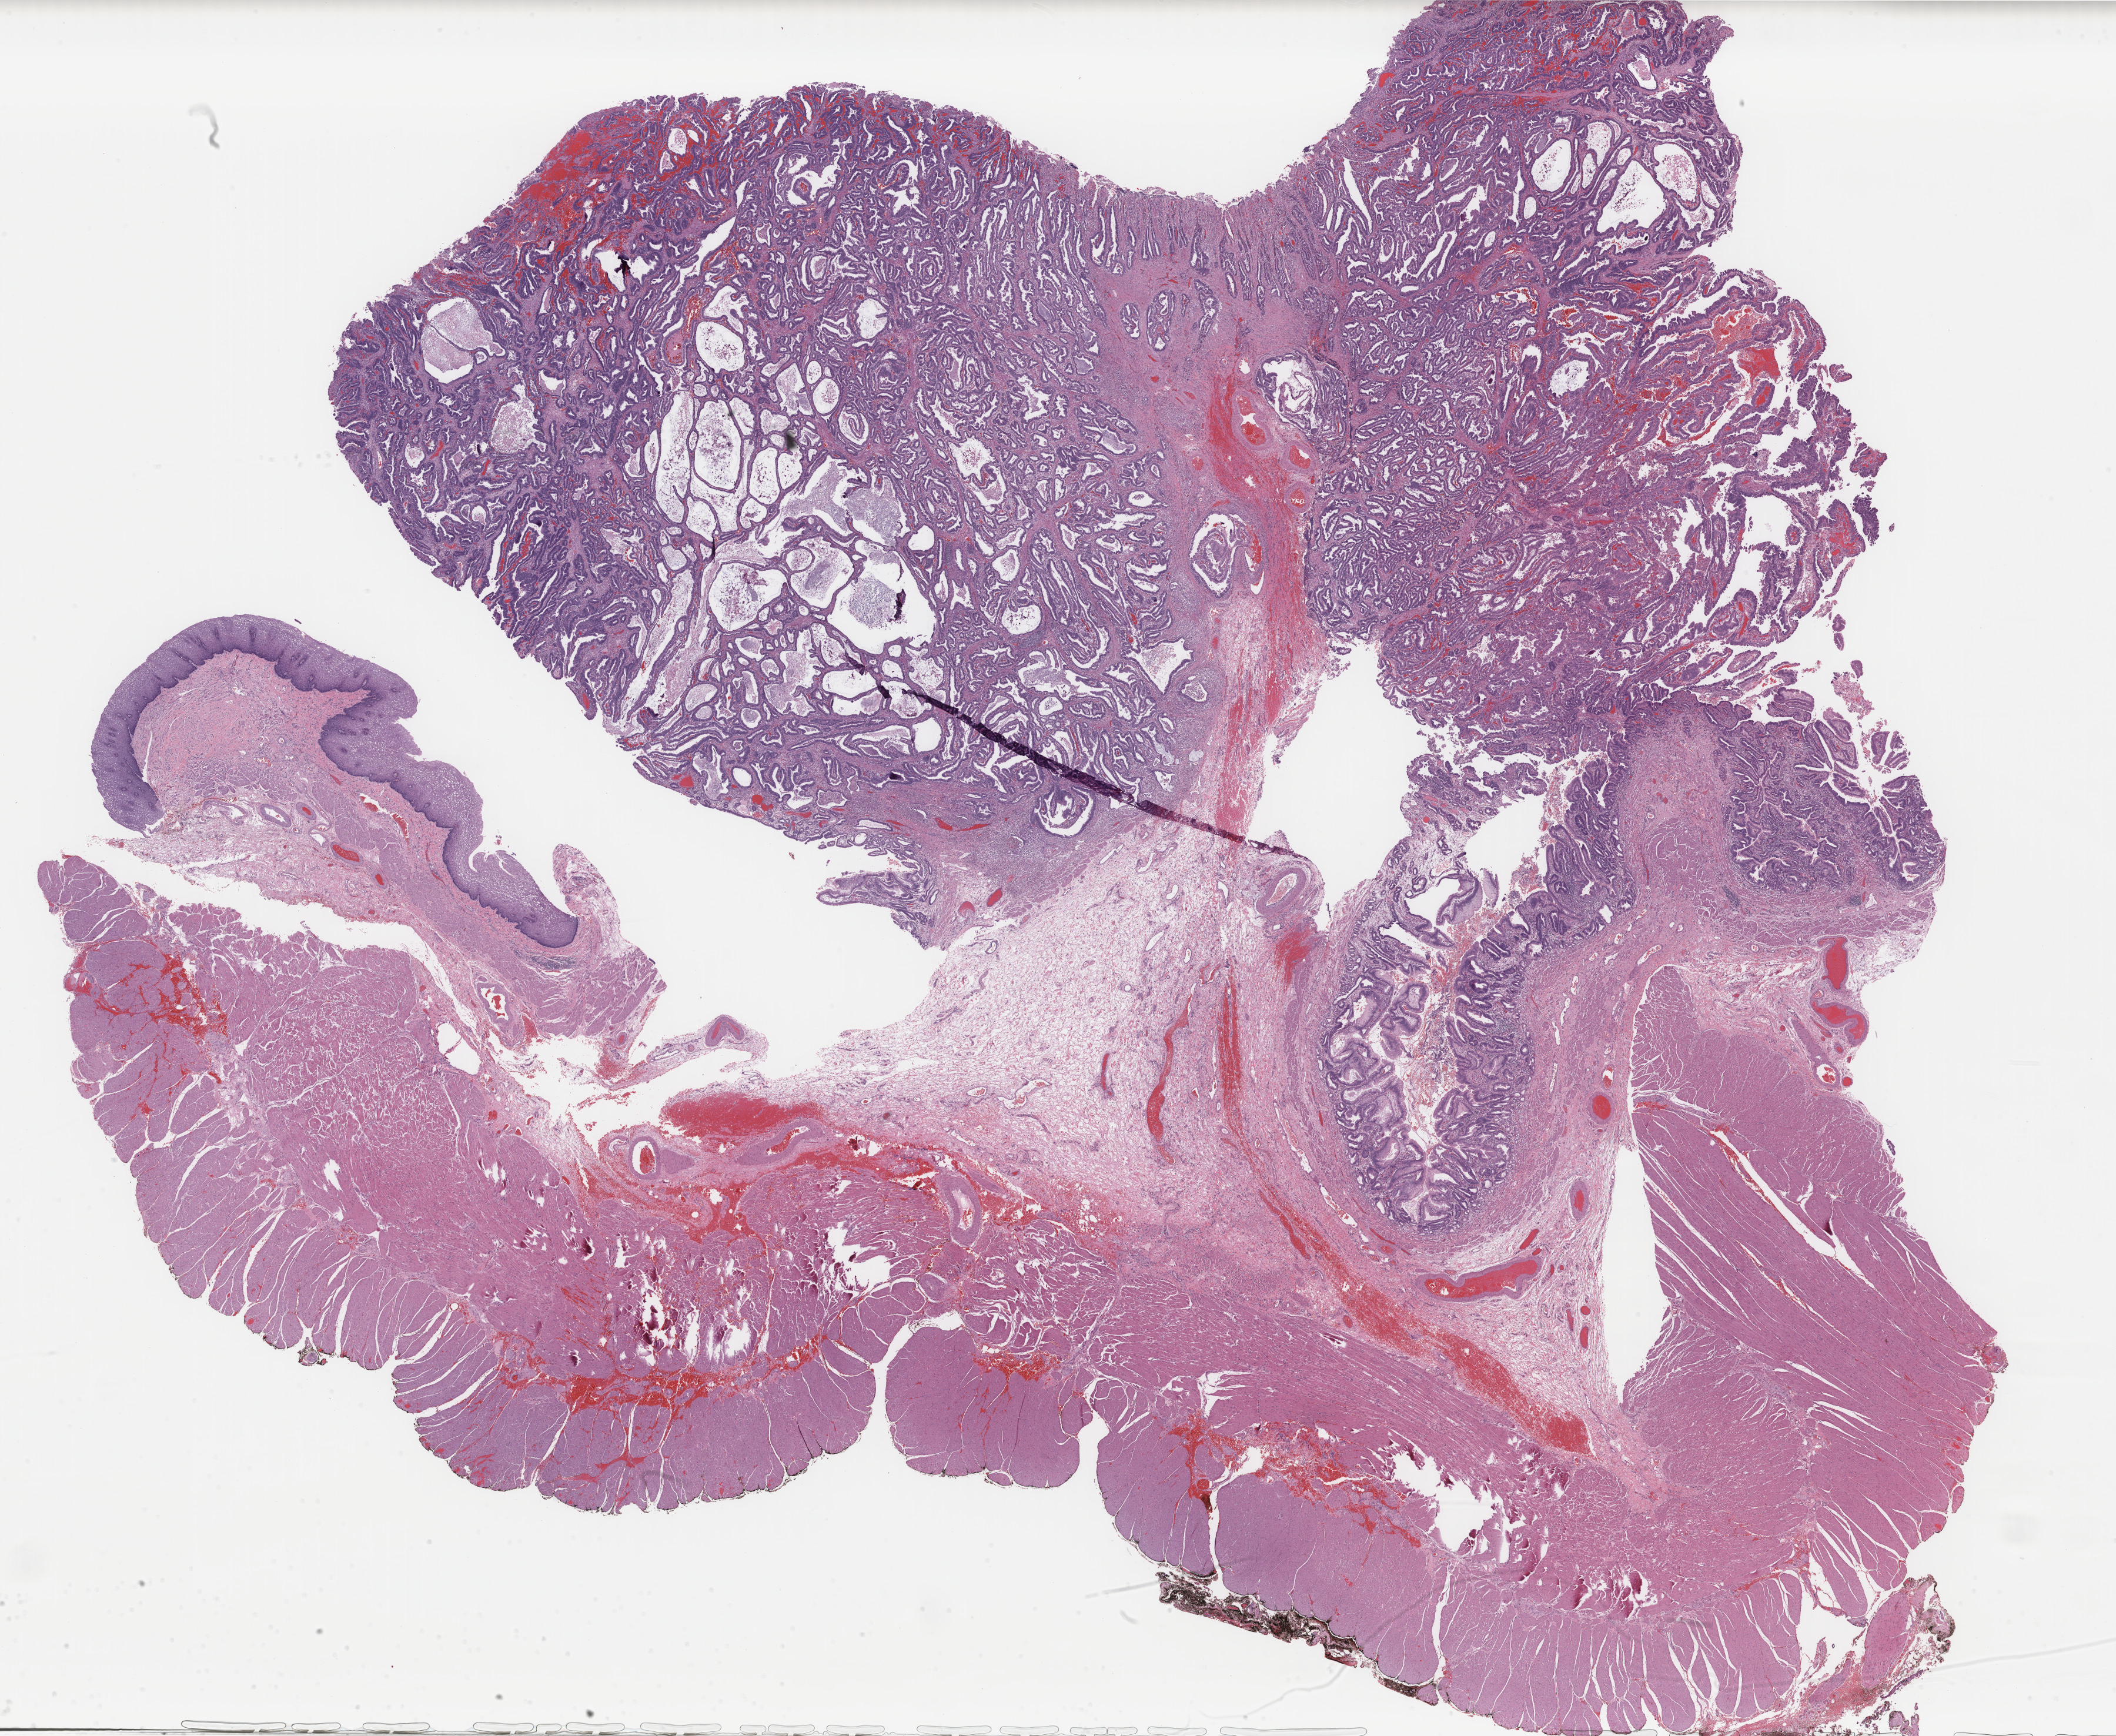
Whole-slide histology image, Hematoxylin and eosin (H&E) stained — low-resolution overview of the scanned area, about 28.6 x 23.4 mm (from a 40x scan). Formalin-fixed paraffin-embedded (FFPE) diagnostic section. Primary tumour sample from the esophagus. Patient: male, age at initial diagnosis 65 years.
Pathologic diagnosis: Adenocarcinoma, NOS (lower third of esophagus).